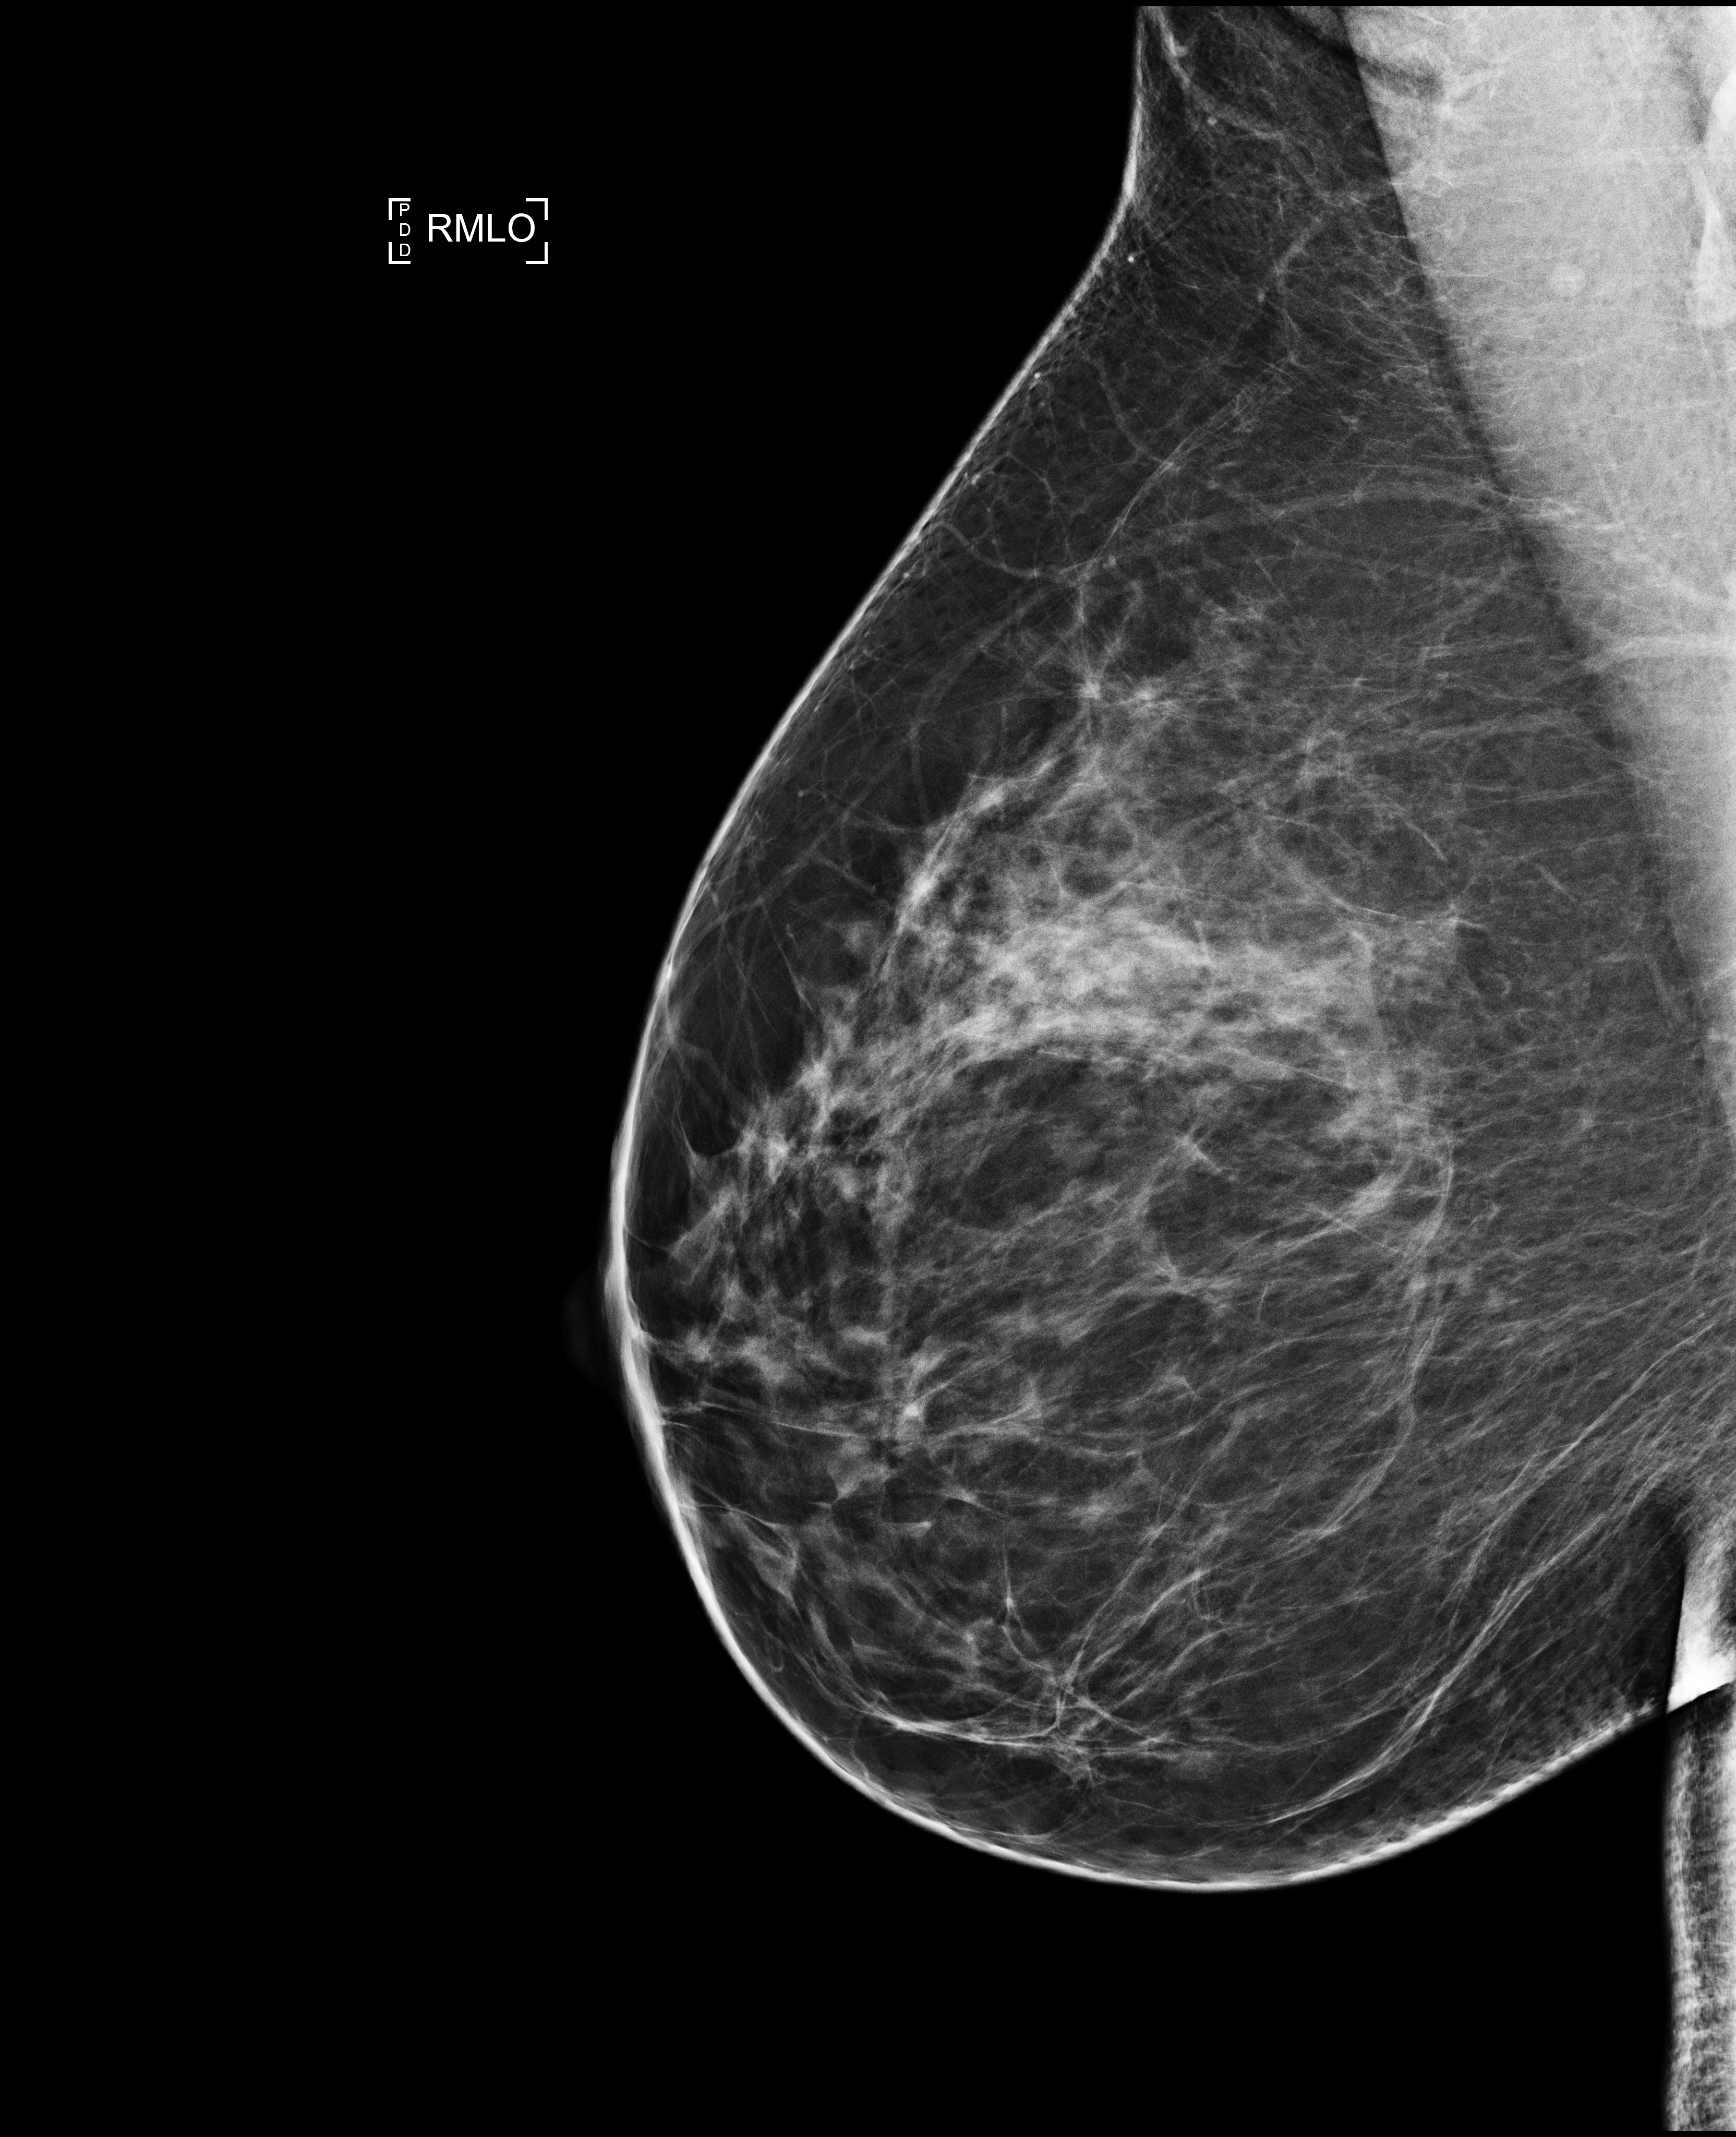
Screening examination. Patient aged 51 years (female).
Image type: full-field digital mammogram. Breast: right. Projection: mediolateral oblique (MLO) view.